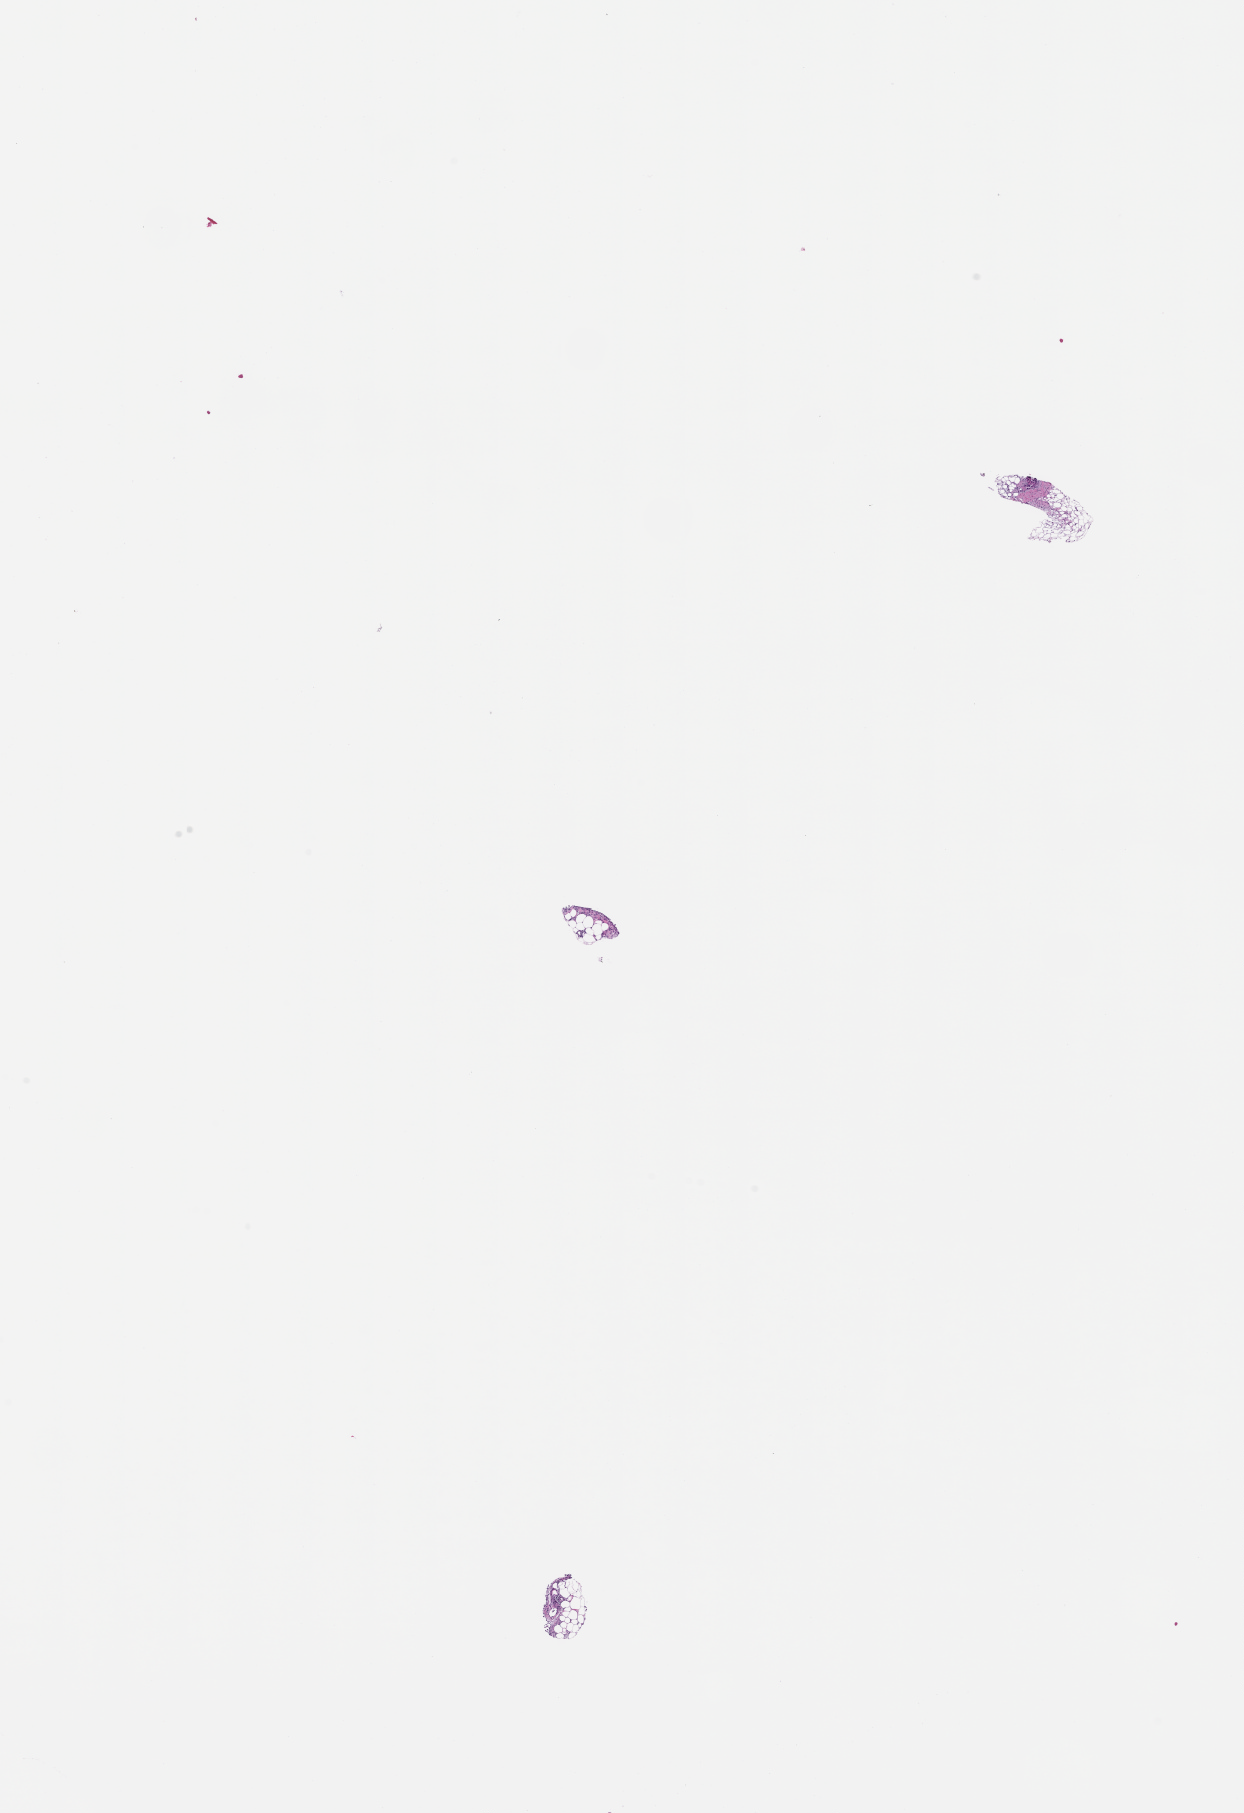
H&E whole-slide image, shown as a low-resolution overview of the whole scanned area (about 10.1 x 14.6 mm). FFPE section. Archival tissue. Patient sex: female.
This section: metastasis (sampled organ not recorded). Patient diagnosis (primary): Ovarian Carcinoma.